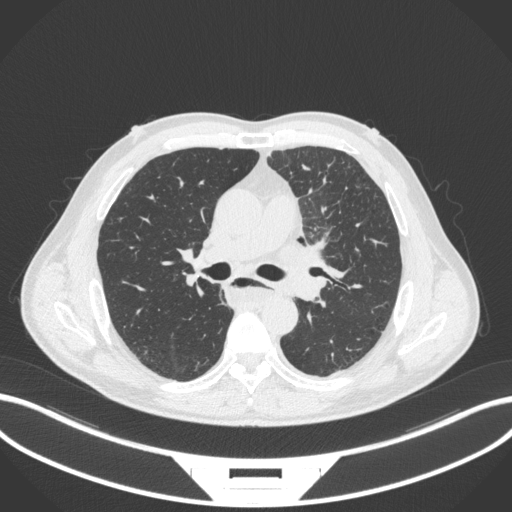
Chest CT, one axial slice; slice 229 of 411 in the series (ordered by position); lung window (W 1500 / L -600 HU); 1 mm slice thickness; 512 × 512 image matrix, field of view 400 × 400 mm. Patient: male, 57 years. Case-level facts recorded for this patient, not image findings: clinical TNM (as recorded): T2a N1 M0.
Annotated regions visible in this slice (bounding box drawn by a radiologist):
- lung tumour (recorded histology: squamous cell carcinoma): bounding box (x1, y1, x2, y2) in pixels: (272, 230, 331, 277)